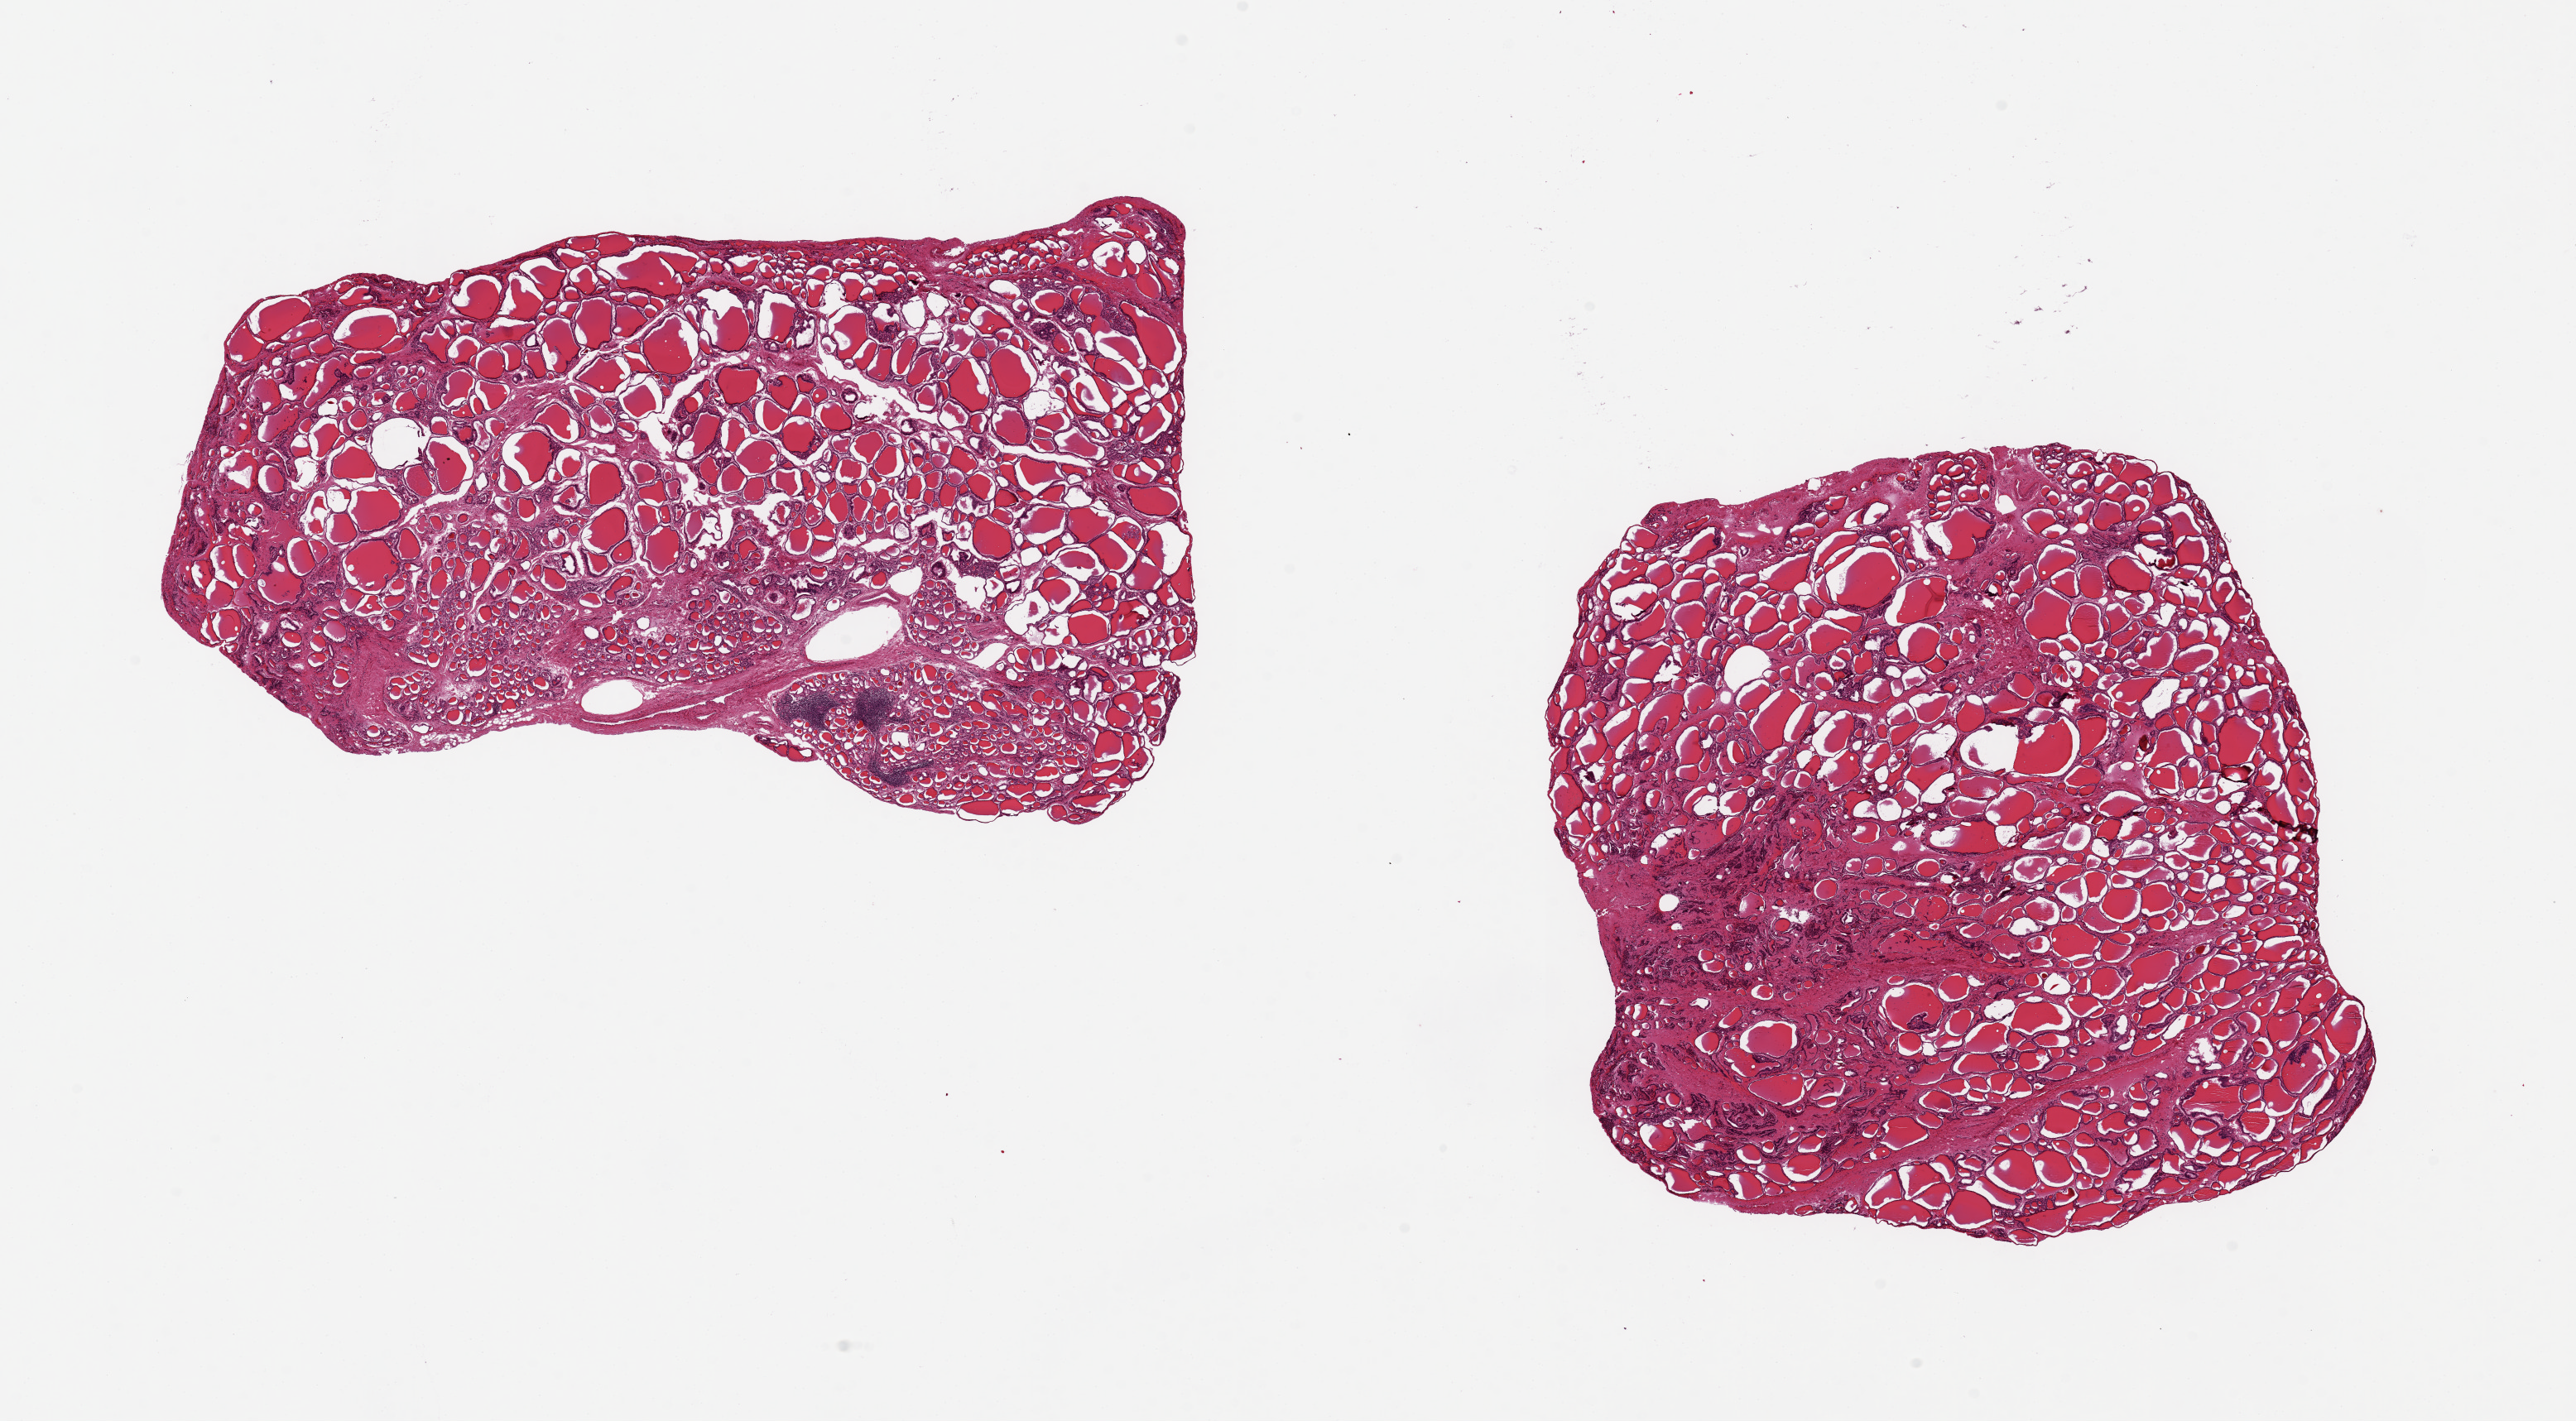
Hematoxylin and eosin (H&E) whole-slide image — low-resolution overview of the scanned area, about 24.6 x 13.6 mm; PAXgene-fixed paraffin-embedded (PFPE) section; sampled site (target tissue): thyroid; donor tissue sample. Donor: female.
* review note (as recorded): 2 pieces ~8x6mm, focal areas of active Hashimoto's thyroiditis, areas of fibrous regression and scarring